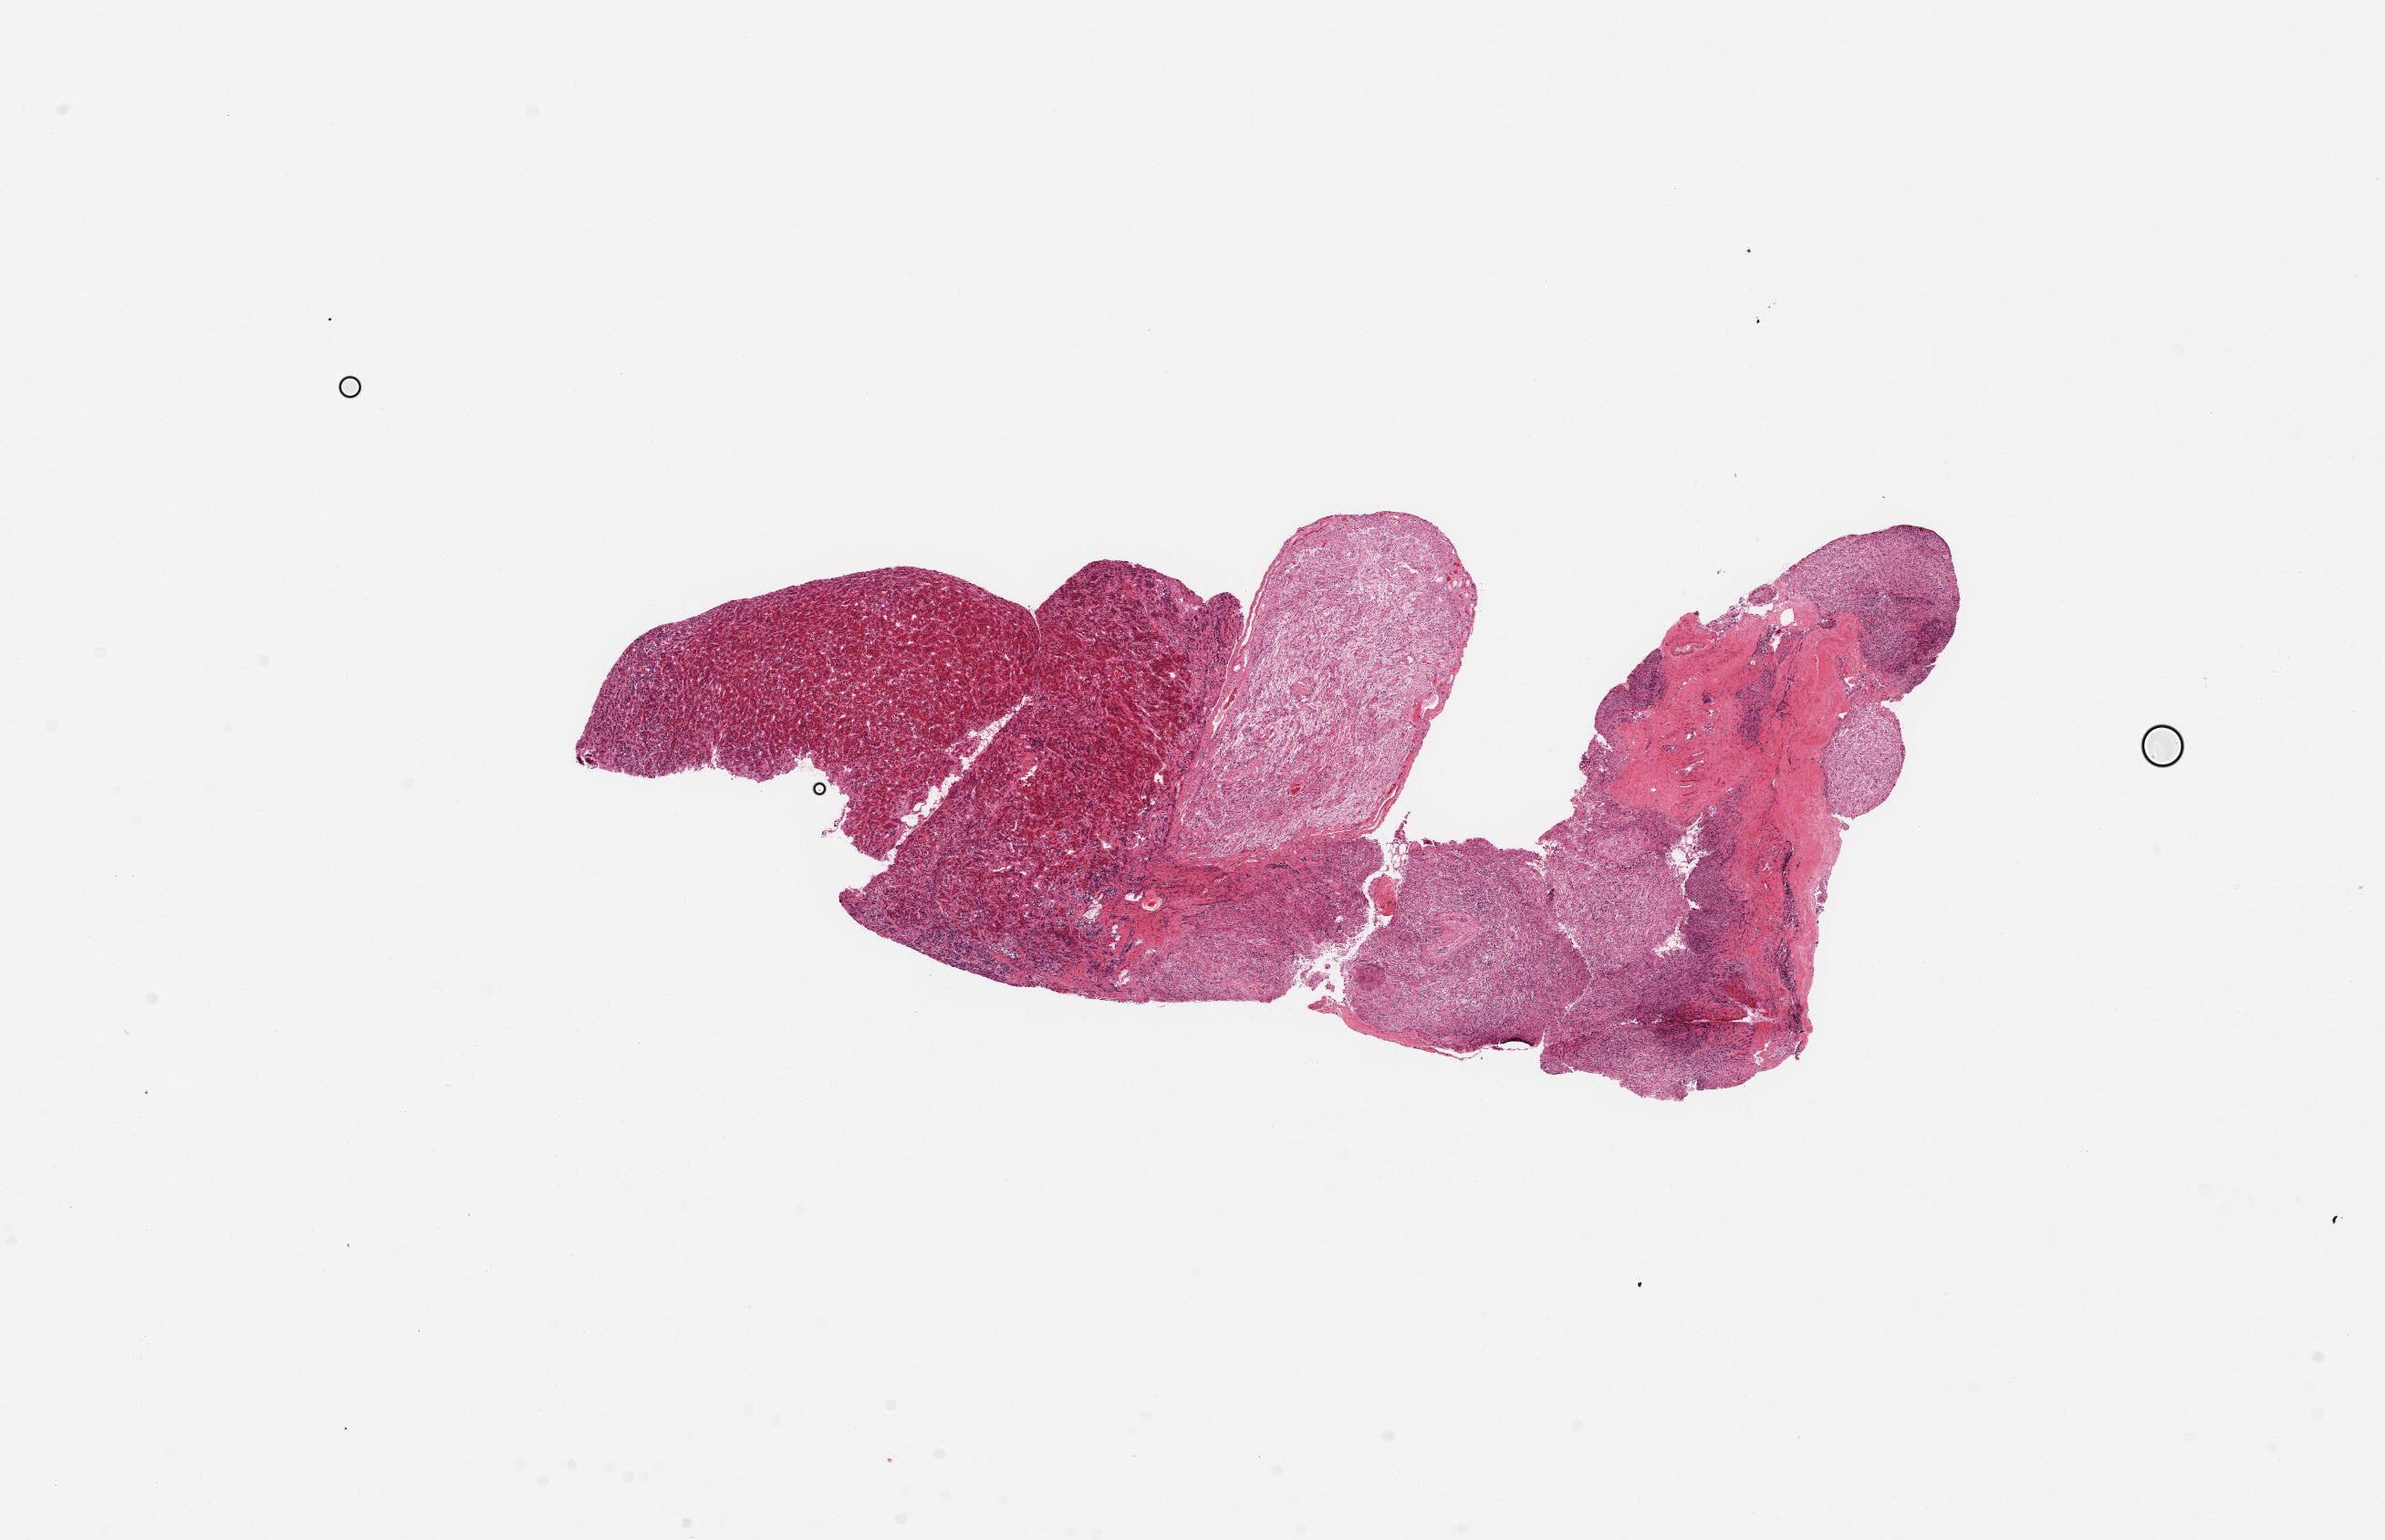
Whole-slide image, H&E stain, brightfield — whole scanned area (about 20.7 x 13.3 mm, slide scanned at 20x) shown as a low-resolution overview. PAXgene-fixed paraffin-embedded (PFPE) section. Sampled site (target tissue): pituitary. Donor tissue sample. Donor sex: female.
Reviewer comment on this tissue sample: 1 piece; anterior and posterior present.